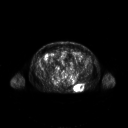
FDG PET of an extremity soft-tissue mass (from a PET/CT study), one axial slice; position 85 of 267 along the scan axis; 3.27 mm slice thickness; 128 × 128 image matrix, field of view 700 × 700 mm. Male patient, age 61 years. From the clinical record (not read from this slice): histological type: pleiomorphic leiomyosarcoma; grade: high; site of the primary tumour: left buttock.
Structures marked on this image (expert contour drawn on MRI and transferred to this co-registered scan by the dataset authors):
- gross tumour volume including surrounding oedema: bounding box <73,84,84,91> (left, top, right, bottom; pixels)
- gross tumour volume (mass): <74,84,84,91>